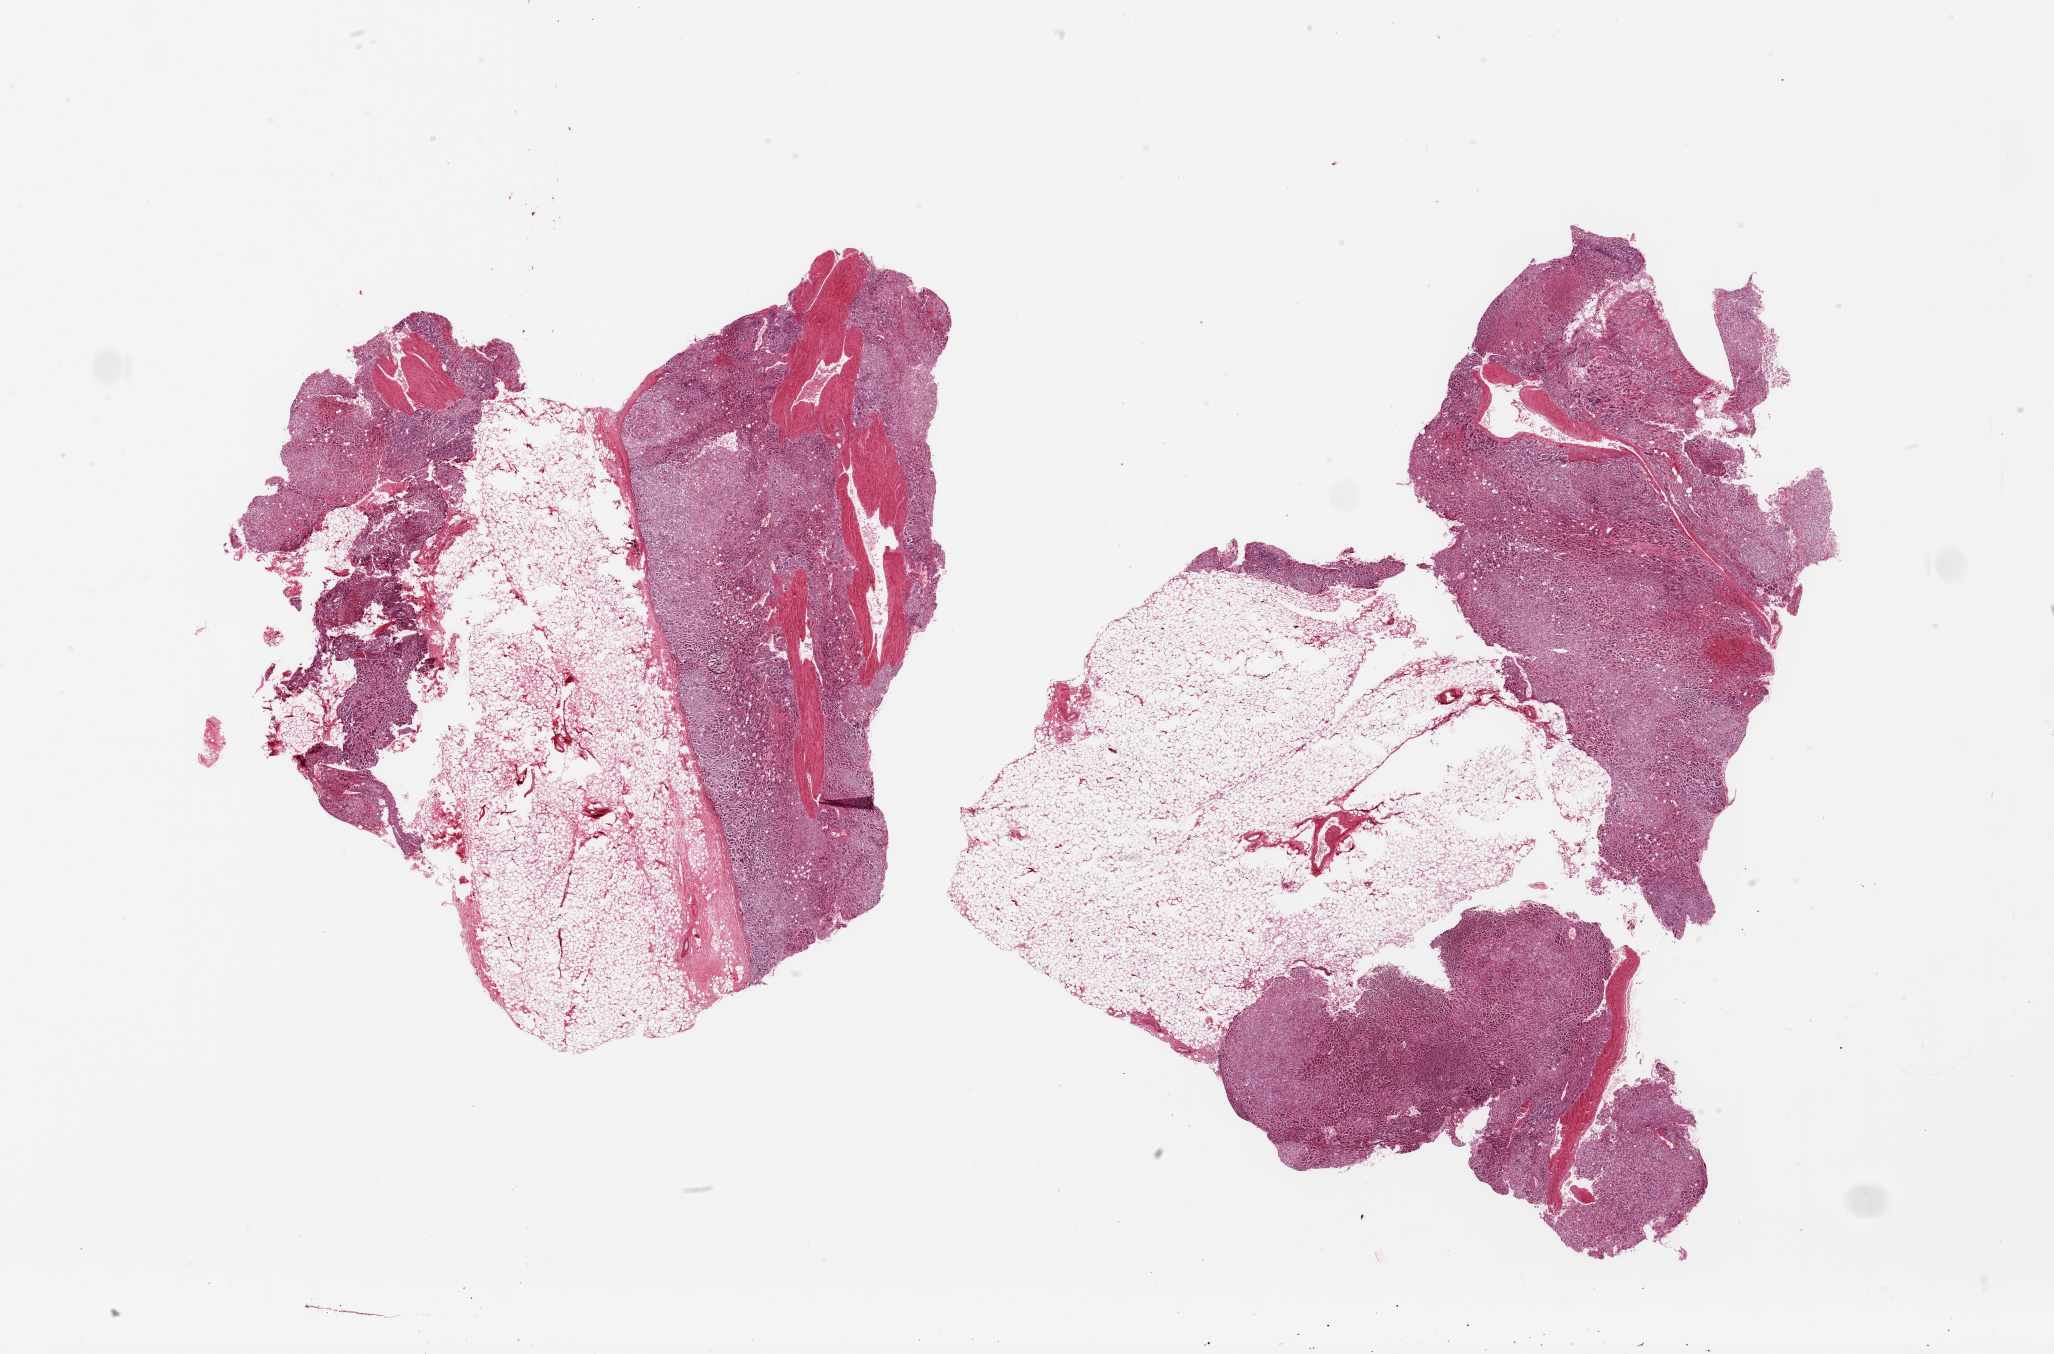
Whole-slide image, haematoxylin and eosin stain, shown as a low-resolution overview of the whole scanned area (about 32.5 x 21.4 mm). PAXgene-fixed paraffin-embedded (PFPE) section. Section of adrenal gland (target tissue). Donor tissue sample. Donor: male.
Reviewer comment on this tissue sample: 2 pieces; both with ~40% attached fat.